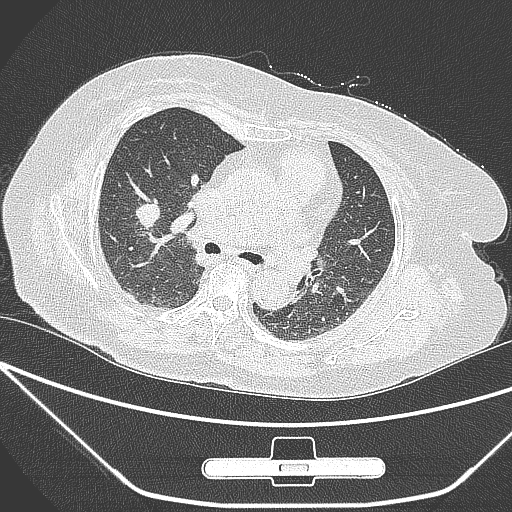
Chest CT, one axial slice; position 161 of 245 along the scan axis; 120 kVp; lung window (W 1500 / L -600 HU); 512 × 512 image matrix, field of view 365 × 365 mm. Patient: female, 65 years. Case-level facts recorded for this patient, not image findings: clinical TNM (as recorded): T1c N0 M0; histopathological grade: G3.
Annotated regions visible in this slice (rectangle marked by the reading radiologist):
- lung tumour (recorded histology: adenocarcinoma): bounding box [x1, y1, x2, y2] px = [132, 193, 172, 230]